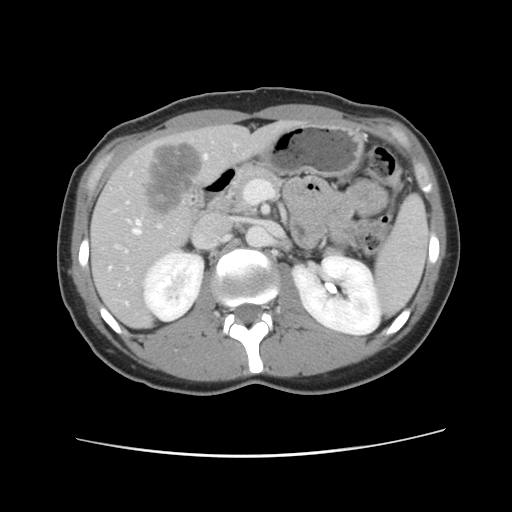
Contrast-enhanced abdominal CT, one axial slice. Slice 51 of 134 in the series (ordered by position). 120 kVp. Soft-tissue window (W 400 / L 40 HU). 2.5 mm slice thickness. 512 × 512 image matrix, field of view 339 × 339 mm. Female patient, age 33 years. Case-level facts recorded for this patient, not image findings: diagnosis: colorectal cancer liver metastases, imaged before liver resection; multiple liver metastases: yes; largest metastasis: 4.5 cm; disease in both lobes: yes.
Outlined on this slice (manually delineated by an expert):
- hepatic veins: bounding box (x1, y1, x2, y2) in pixels: (110, 156, 208, 269)
- liver: (91, 122, 295, 328)
- planned liver remnant (the part of the liver to remain after resection): (92, 122, 294, 328)
- liver metastasis: (141, 140, 206, 219)